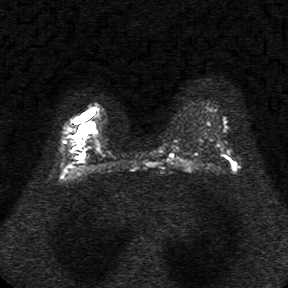
Breast MRI, one axial slice; position 23 of 34 along the scan axis; diffusion-weighted series; image 2 of 4 stored at this slice position (different b-values; order by instance number); 1.5 T; 5 mm slice thickness; 288 × 288 image matrix, field of view 340 × 340 mm. Female patient.
Structures marked on this image (outlined manually by an expert reader):
- tumour on diffusion-weighted imaging: box from (x=73, y=104) to (x=100, y=138) px